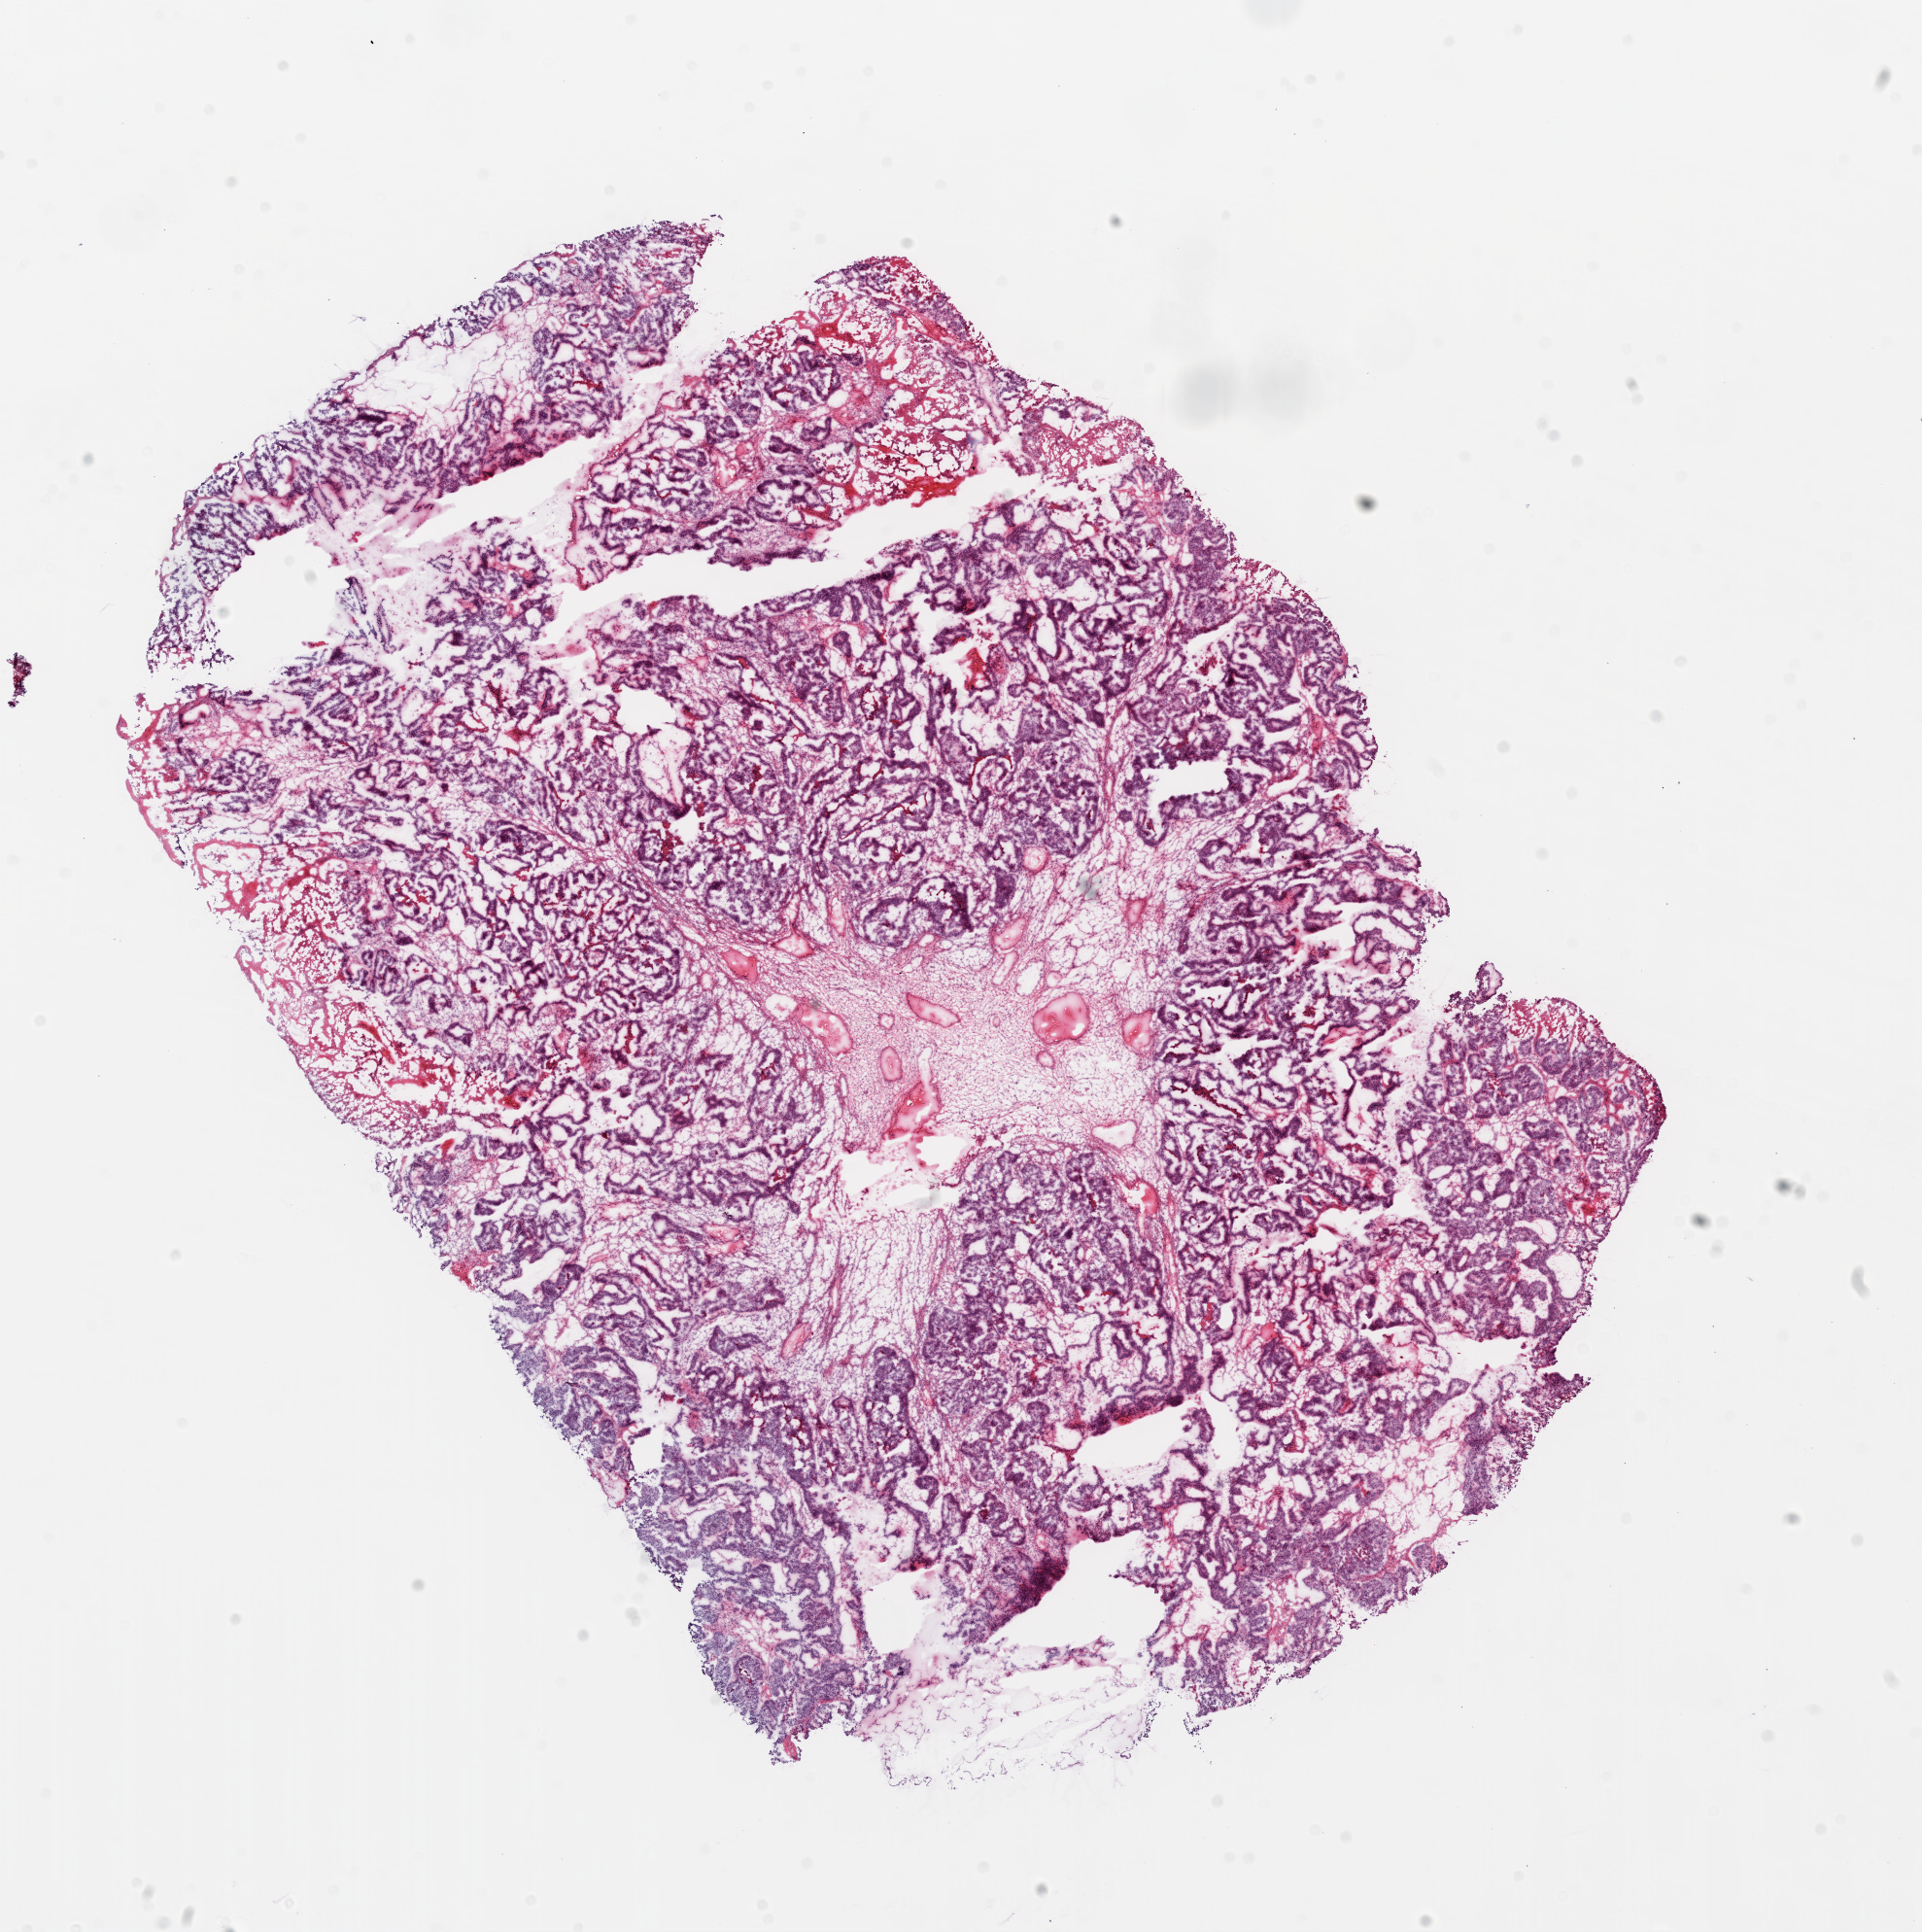
Whole-slide histology image, H&E-stained, a low-resolution overview of the entire scanned area, about 16.0 x 16.0 mm. Slide review estimates, as recorded: tumour cells 80%, tumour nuclei 90%.
Specimen: frozen section from the top of the tissue portion; ovary, primary tumour sample.